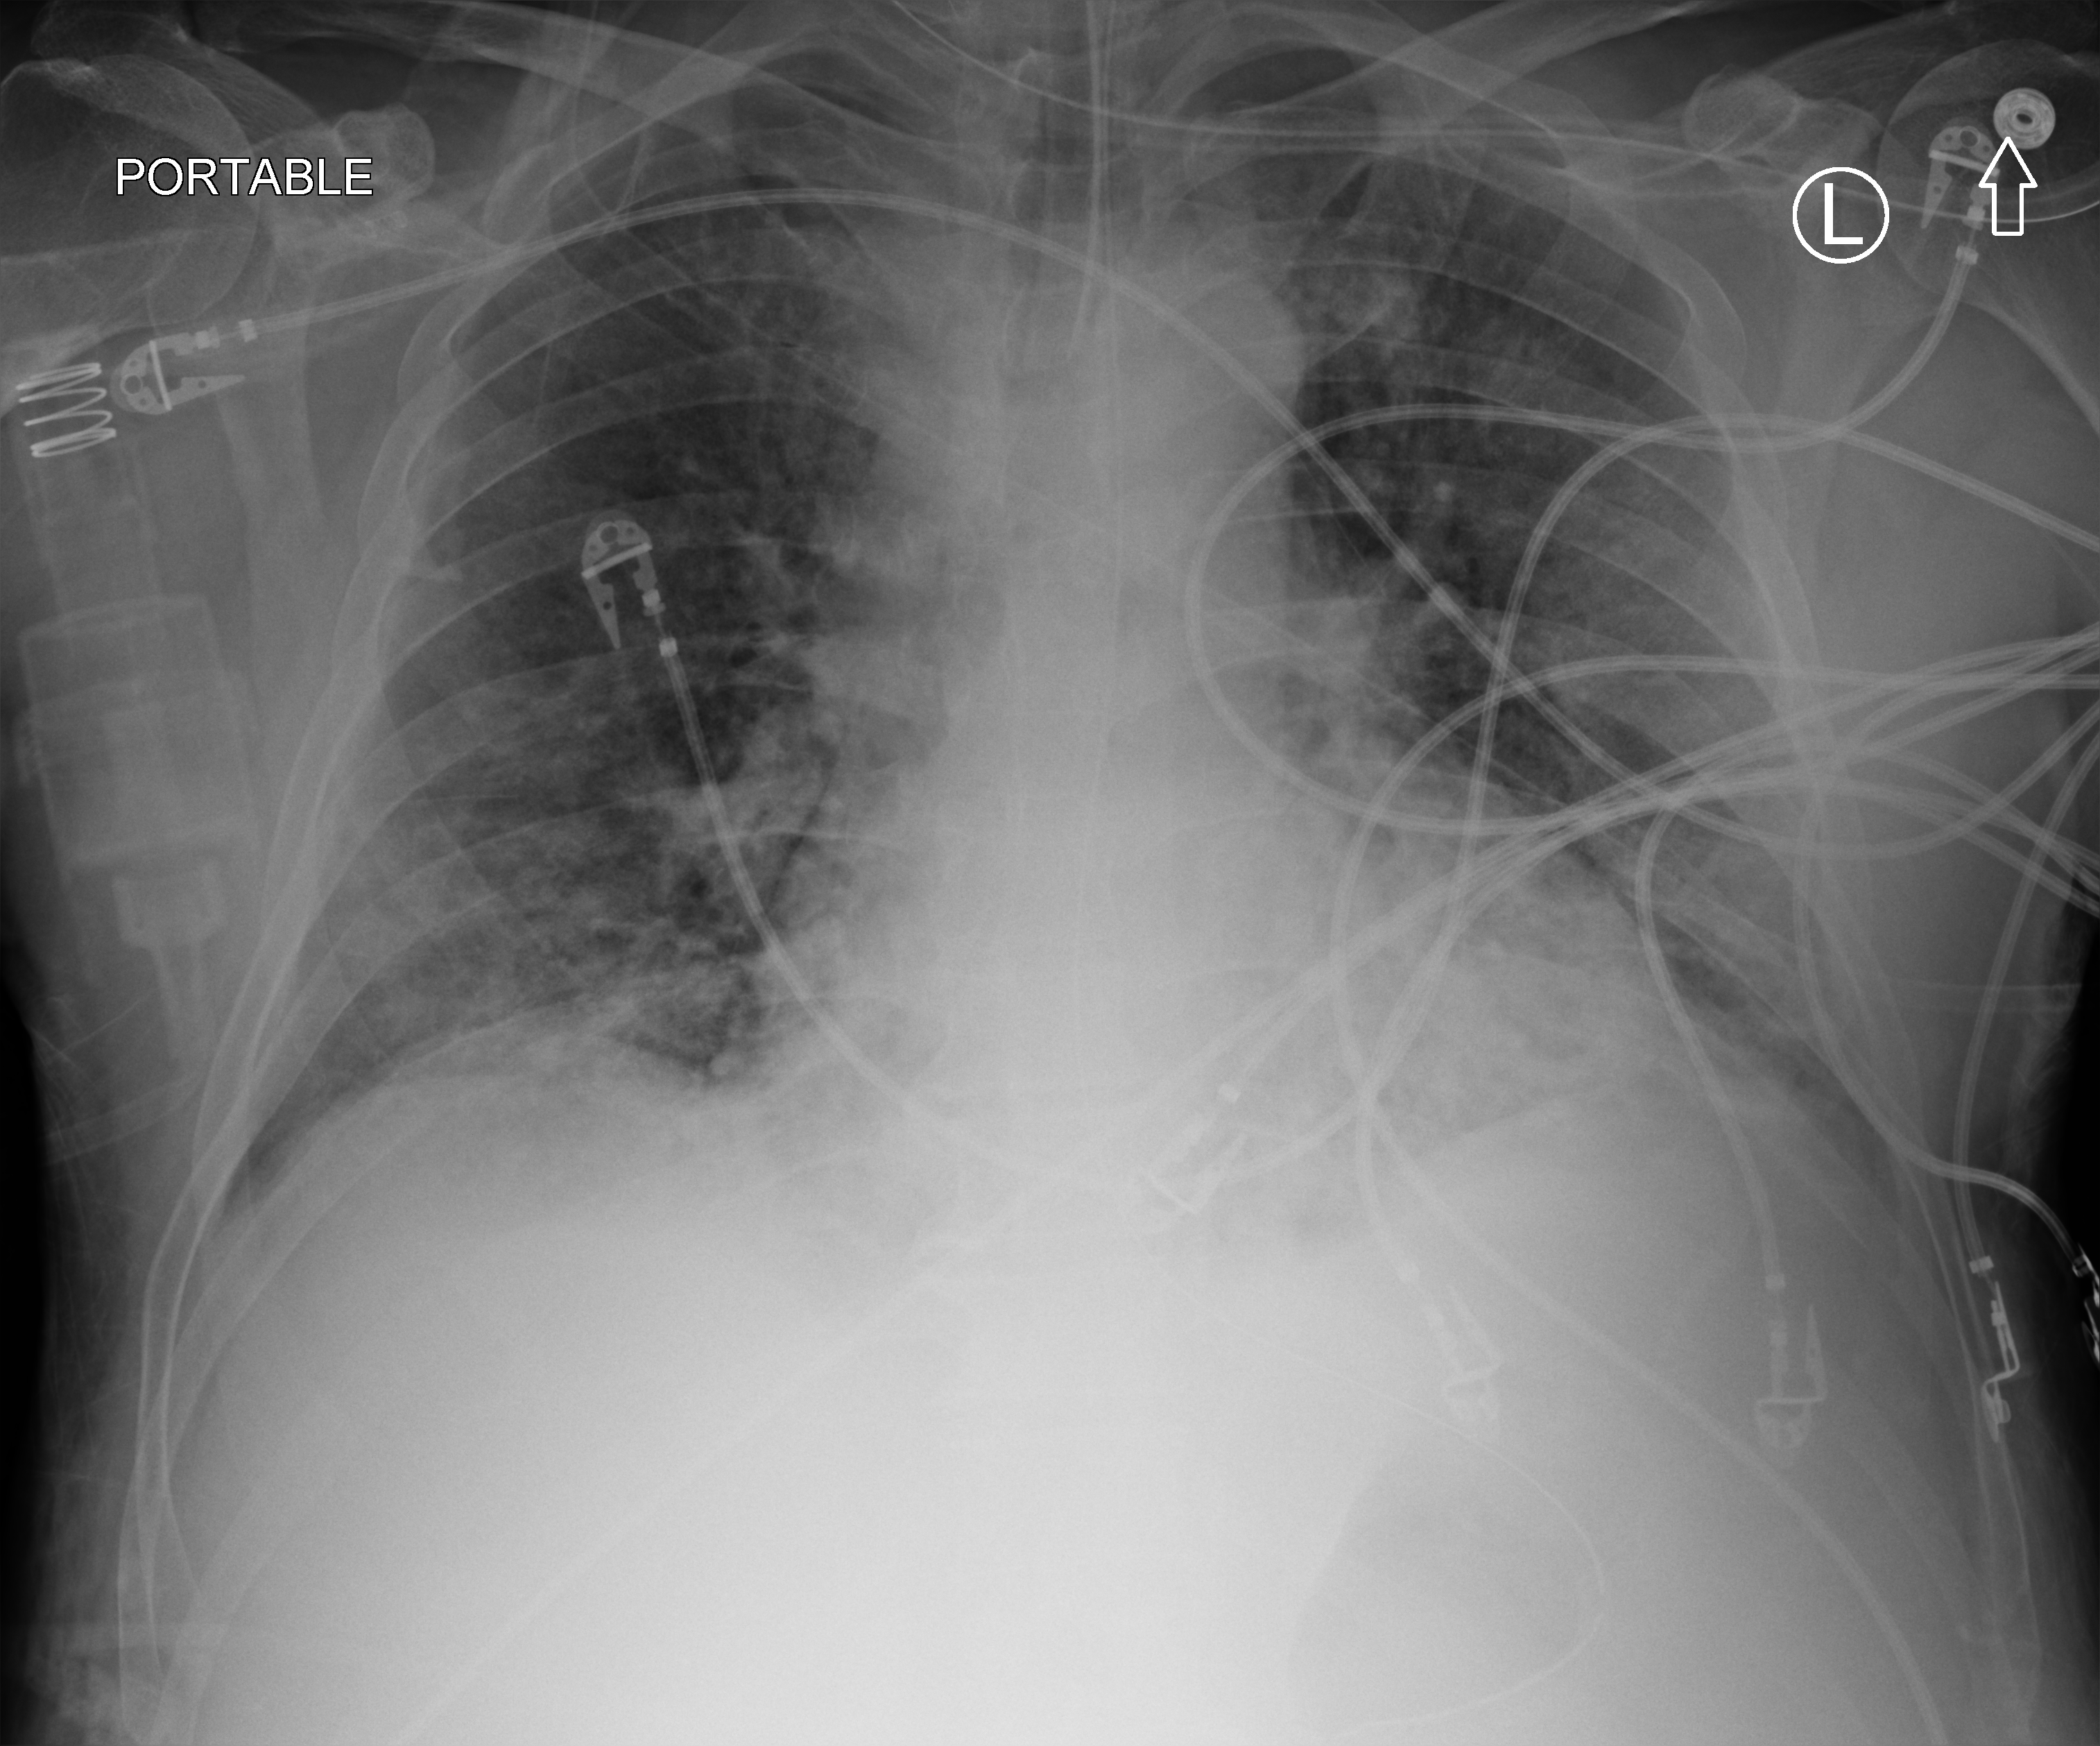
Portable chest radiograph, anteroposterior (AP) projection. Male patient hospitalised with COVID-19, age 18–59 years.
Admission-level facts for this patient (not findings on this image; timing relative to this image not recorded):
- mechanically ventilated during this hospital stay: yes
- hypertension (admission record): no